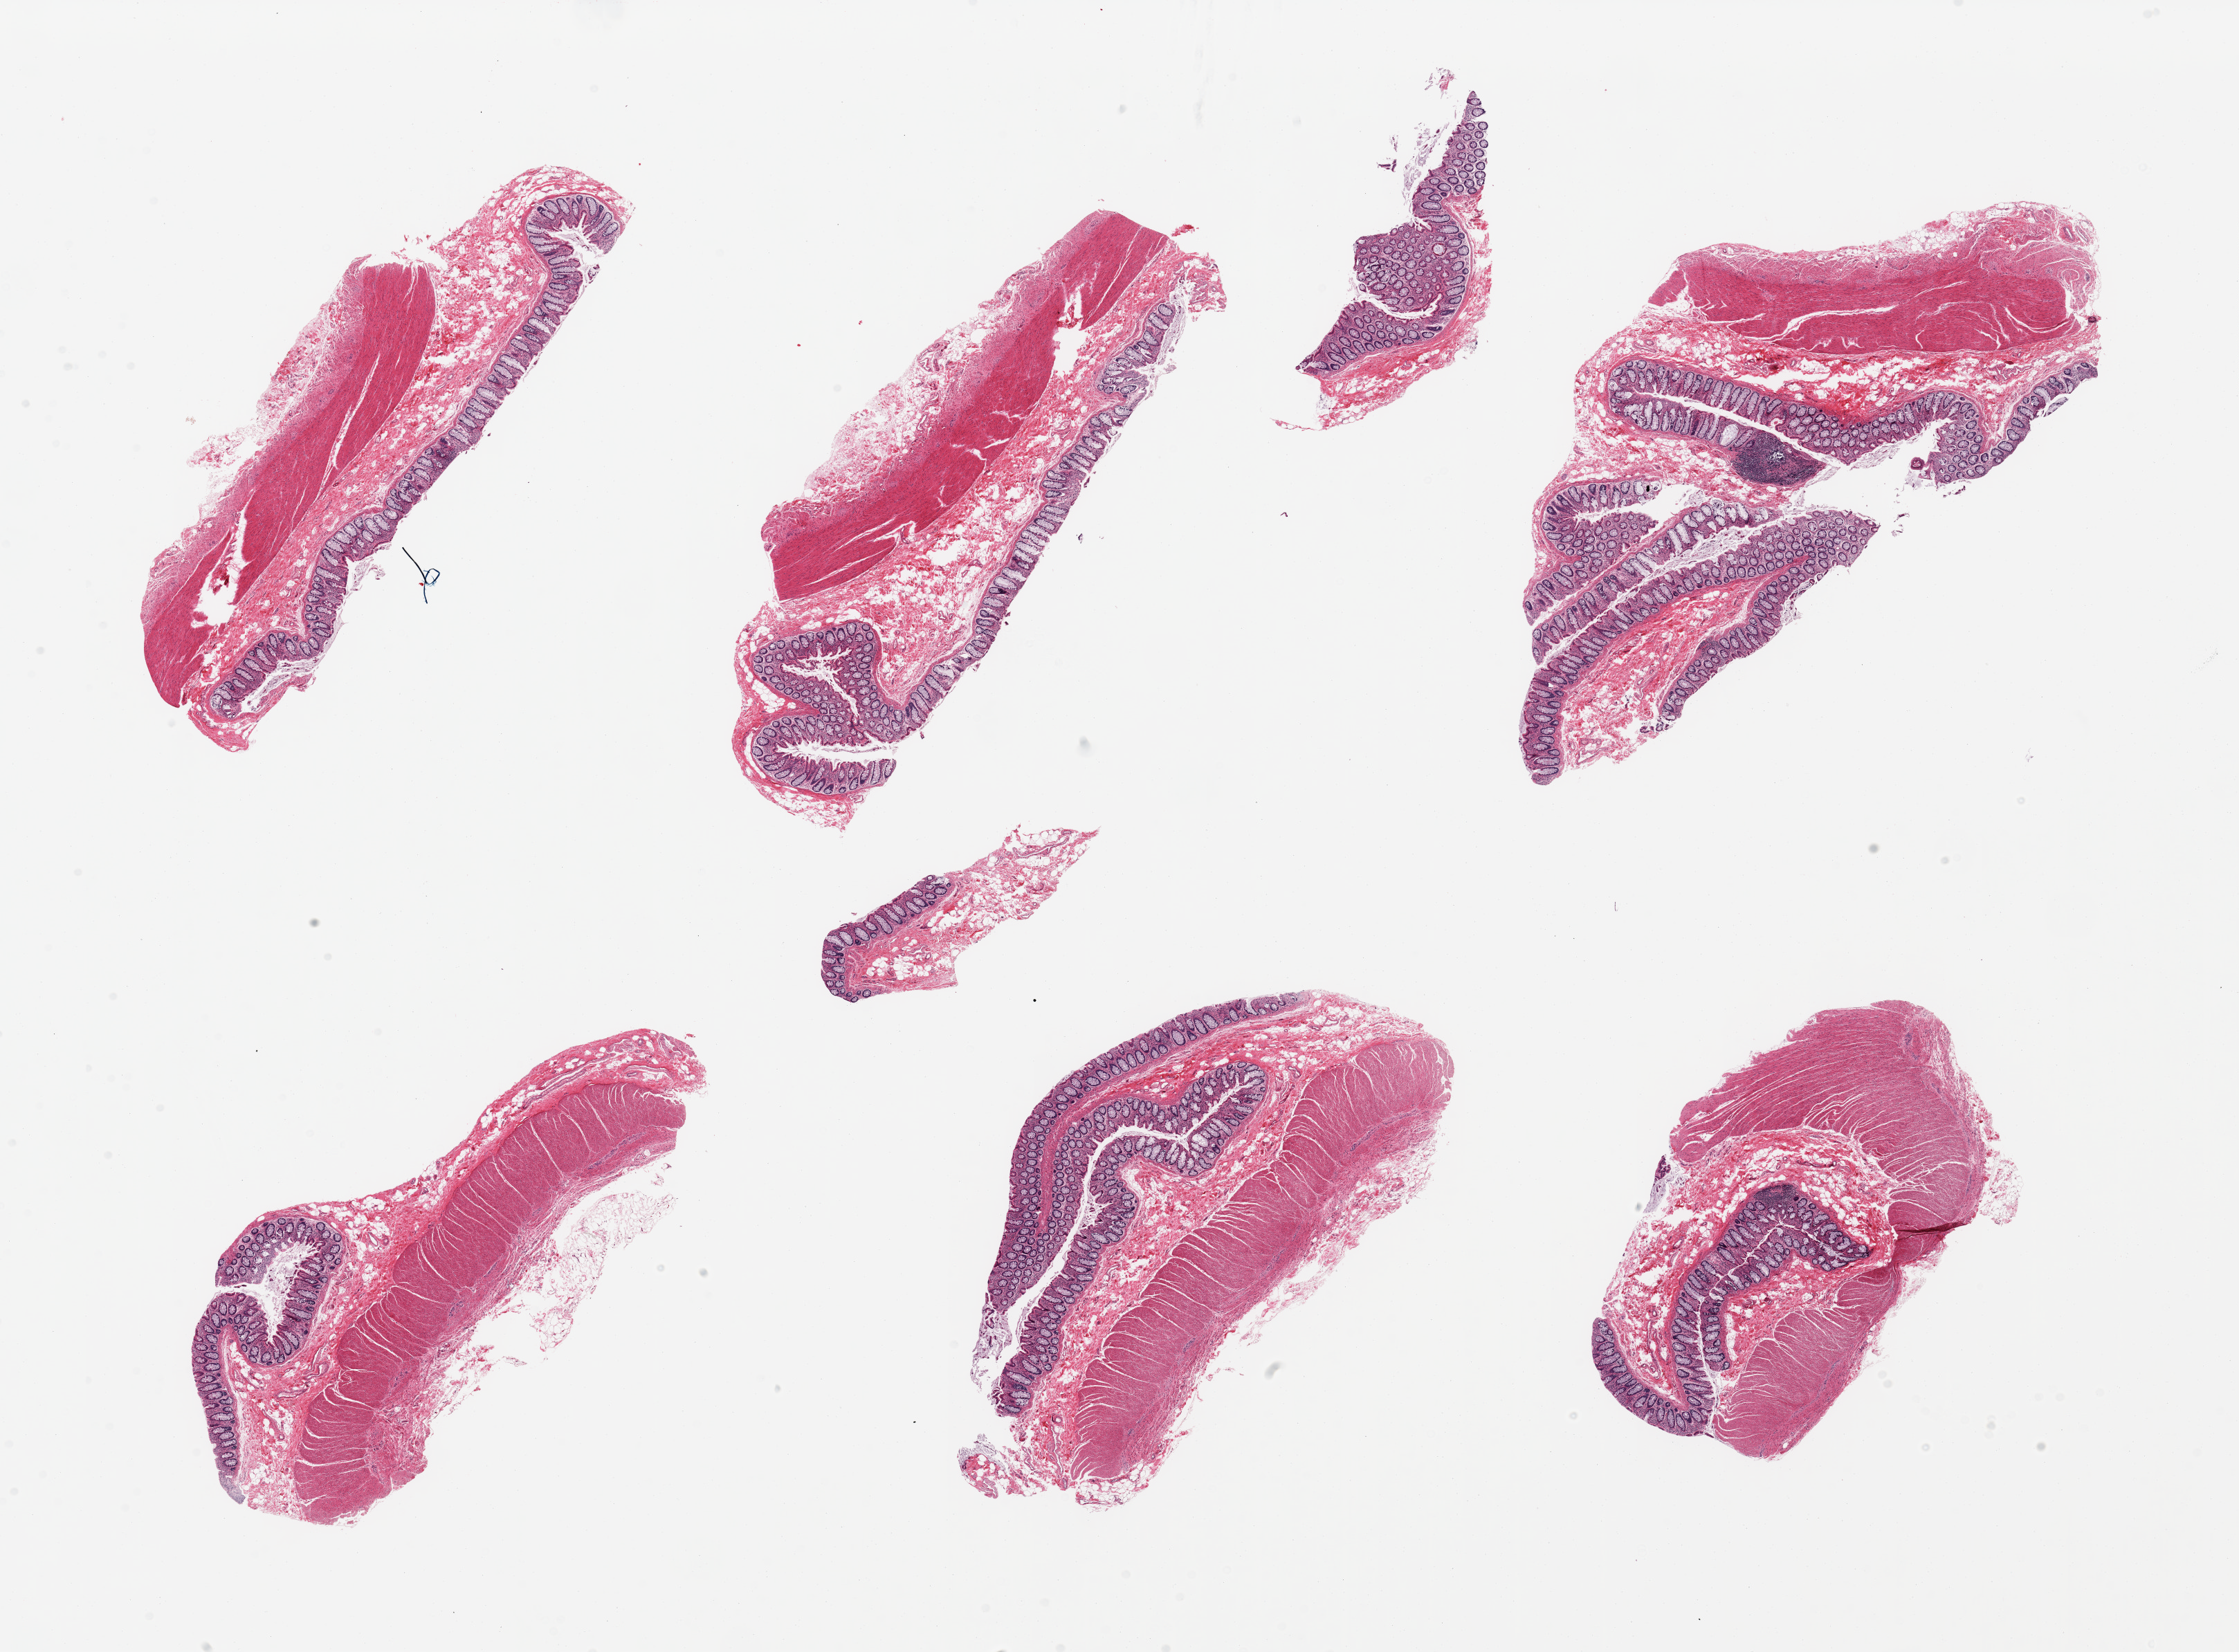
Whole-slide image, haematoxylin and eosin stain, shown as a low-resolution overview of the whole scanned area (about 25.6 x 18.9 mm, from a 20x scan). PAXgene-fixed, paraffin-embedded tissue. Sampled site (target tissue): sigmoid colon. Donor tissue sample. Donor sex: male.
Reviewer comment on this tissue sample: 6 pieces, abundant mucosa, not correct target.